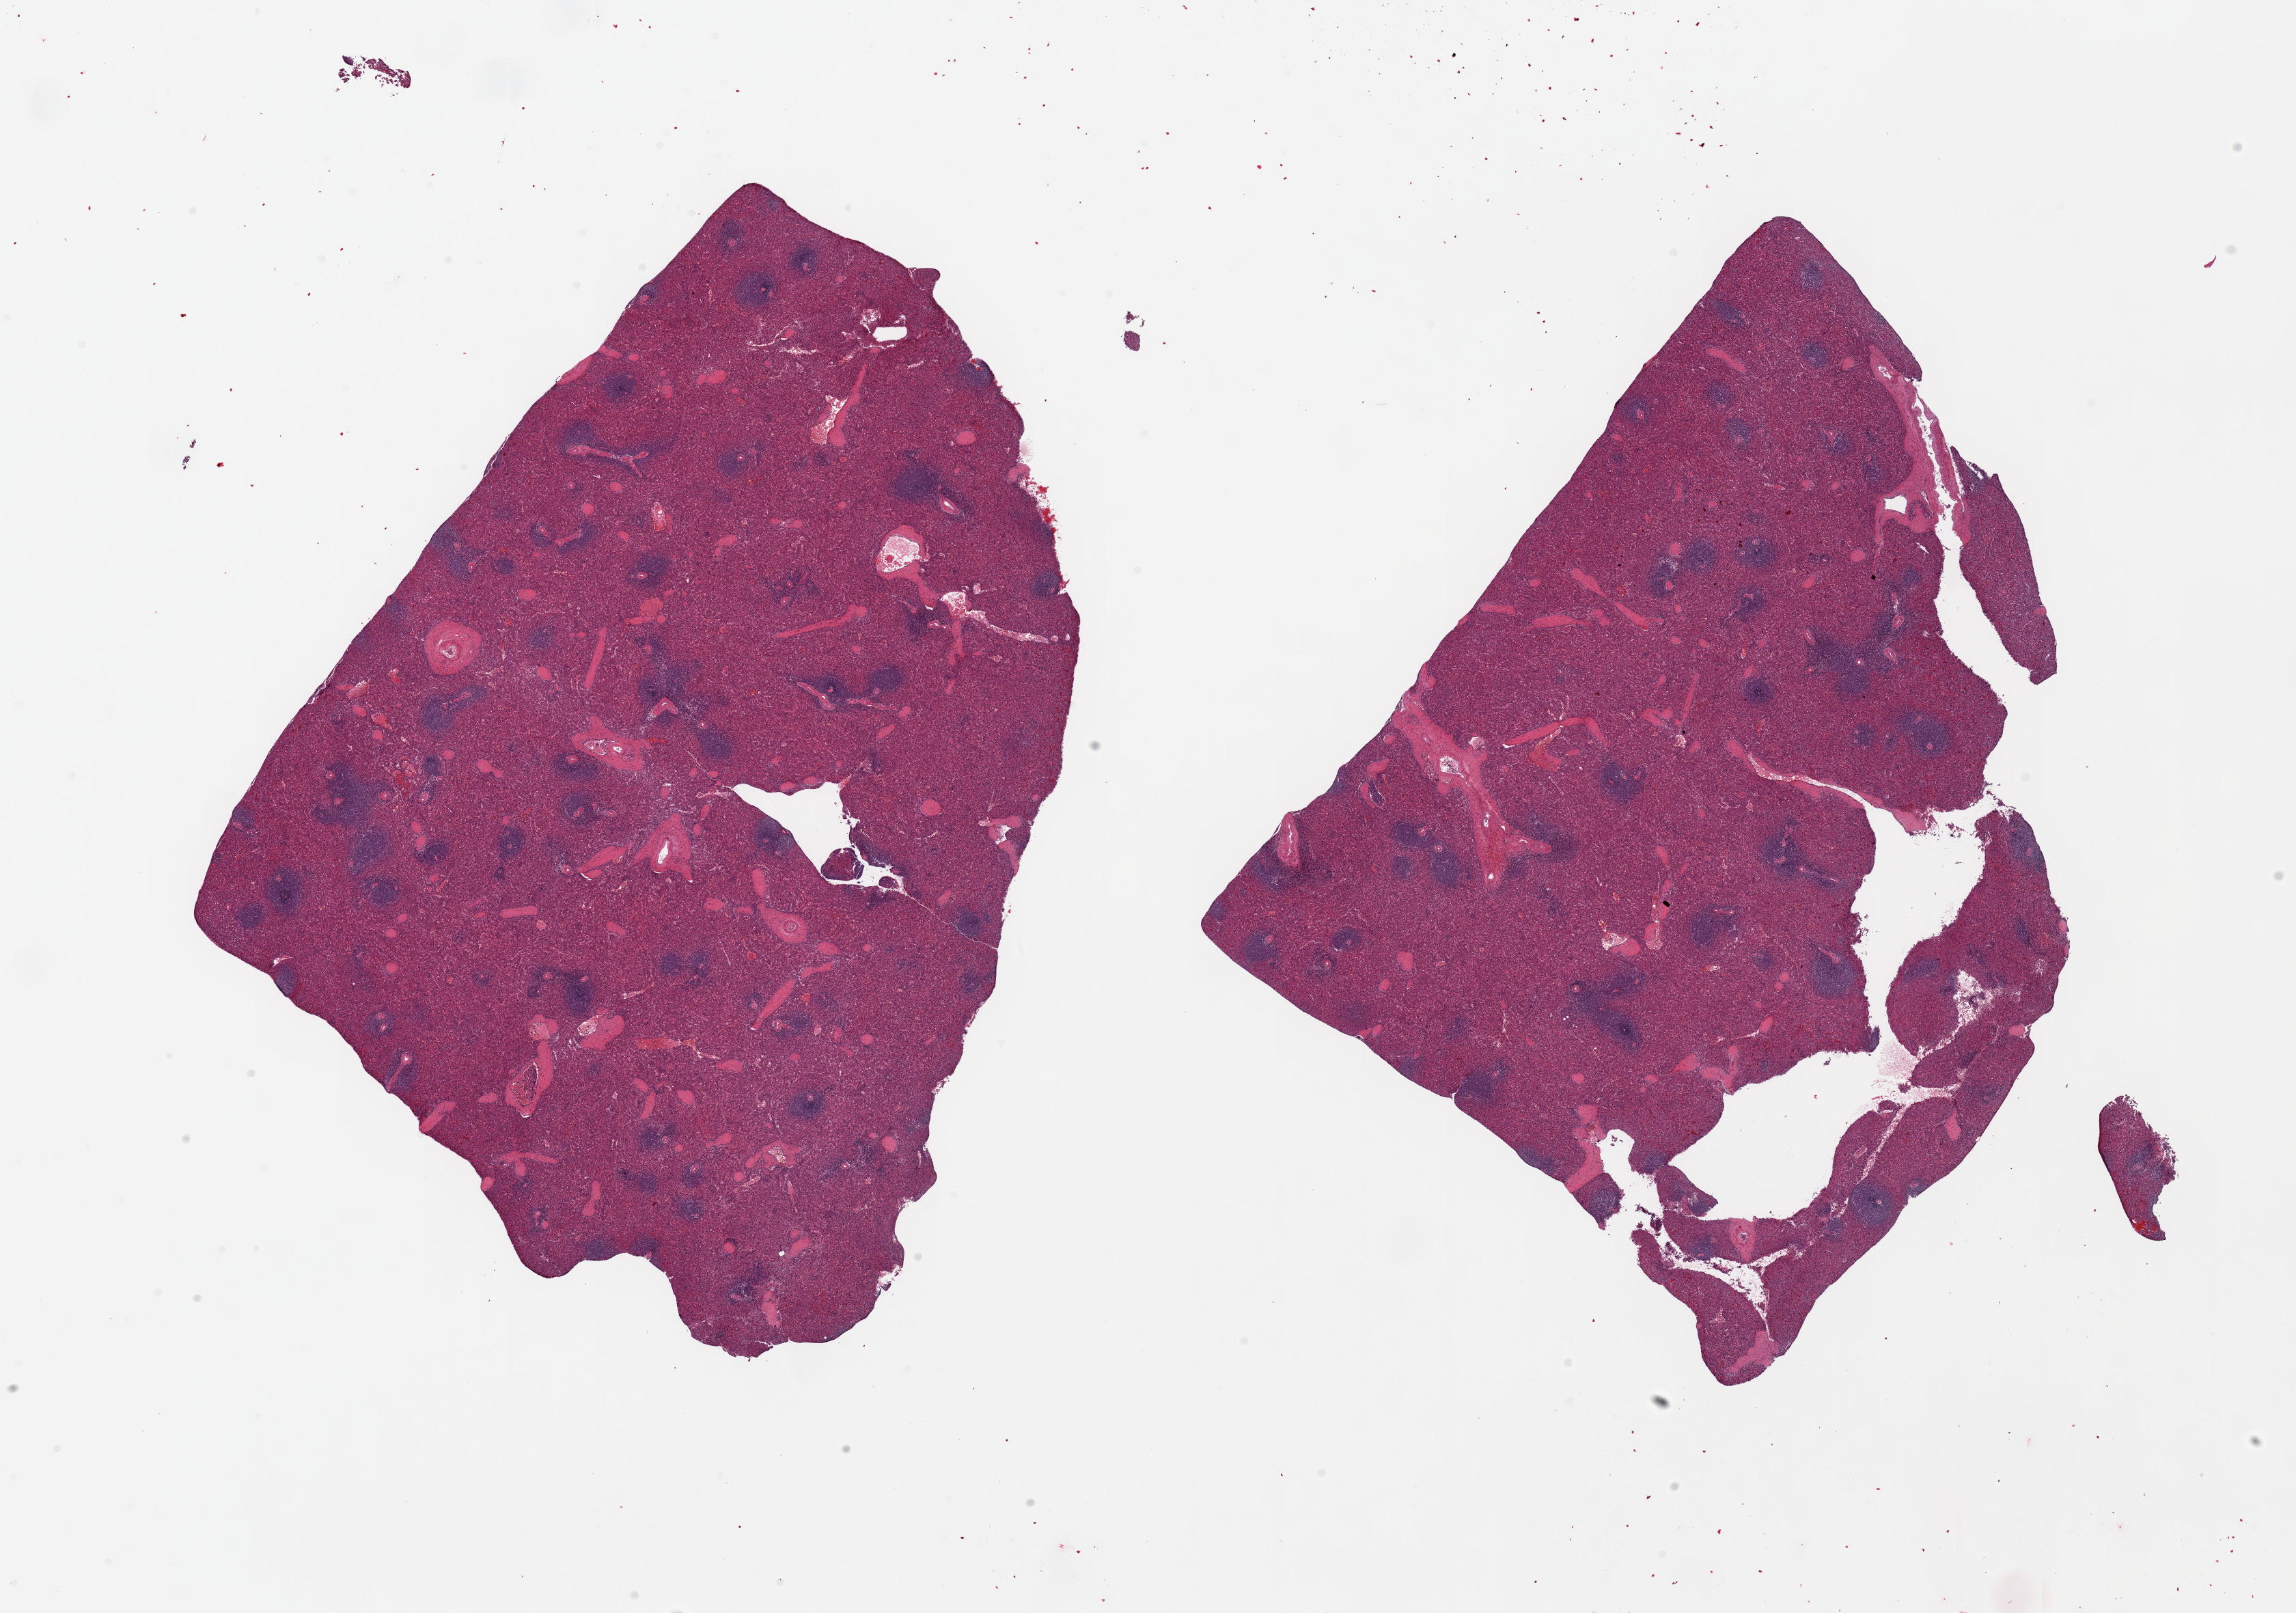
Digitized haematoxylin and eosin-stained section, brightfield, low-resolution overview of the scanned area, about 26.6 x 18.7 mm (from a 20x scan), PAXgene-fixed paraffin-embedded (PFPE) section, target tissue: spleen, donor tissue sample.
Review note (as recorded): 2 pieces.